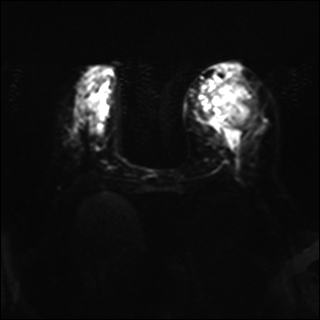
Breast MRI, one axial slice; slice 14 of 37 in the series (ordered by position); diffusion-weighted series; image 2 of 4 stored at this slice position (different b-values; order by instance number); 1.5 T; 4 mm slice thickness; 320 × 320 image matrix, field of view 320 × 320 mm. Female patient.
Annotated regions visible in this slice (manually delineated by an expert):
- tumour on diffusion-weighted imaging: bounding box <210,81,256,128> (left, top, right, bottom; pixels)